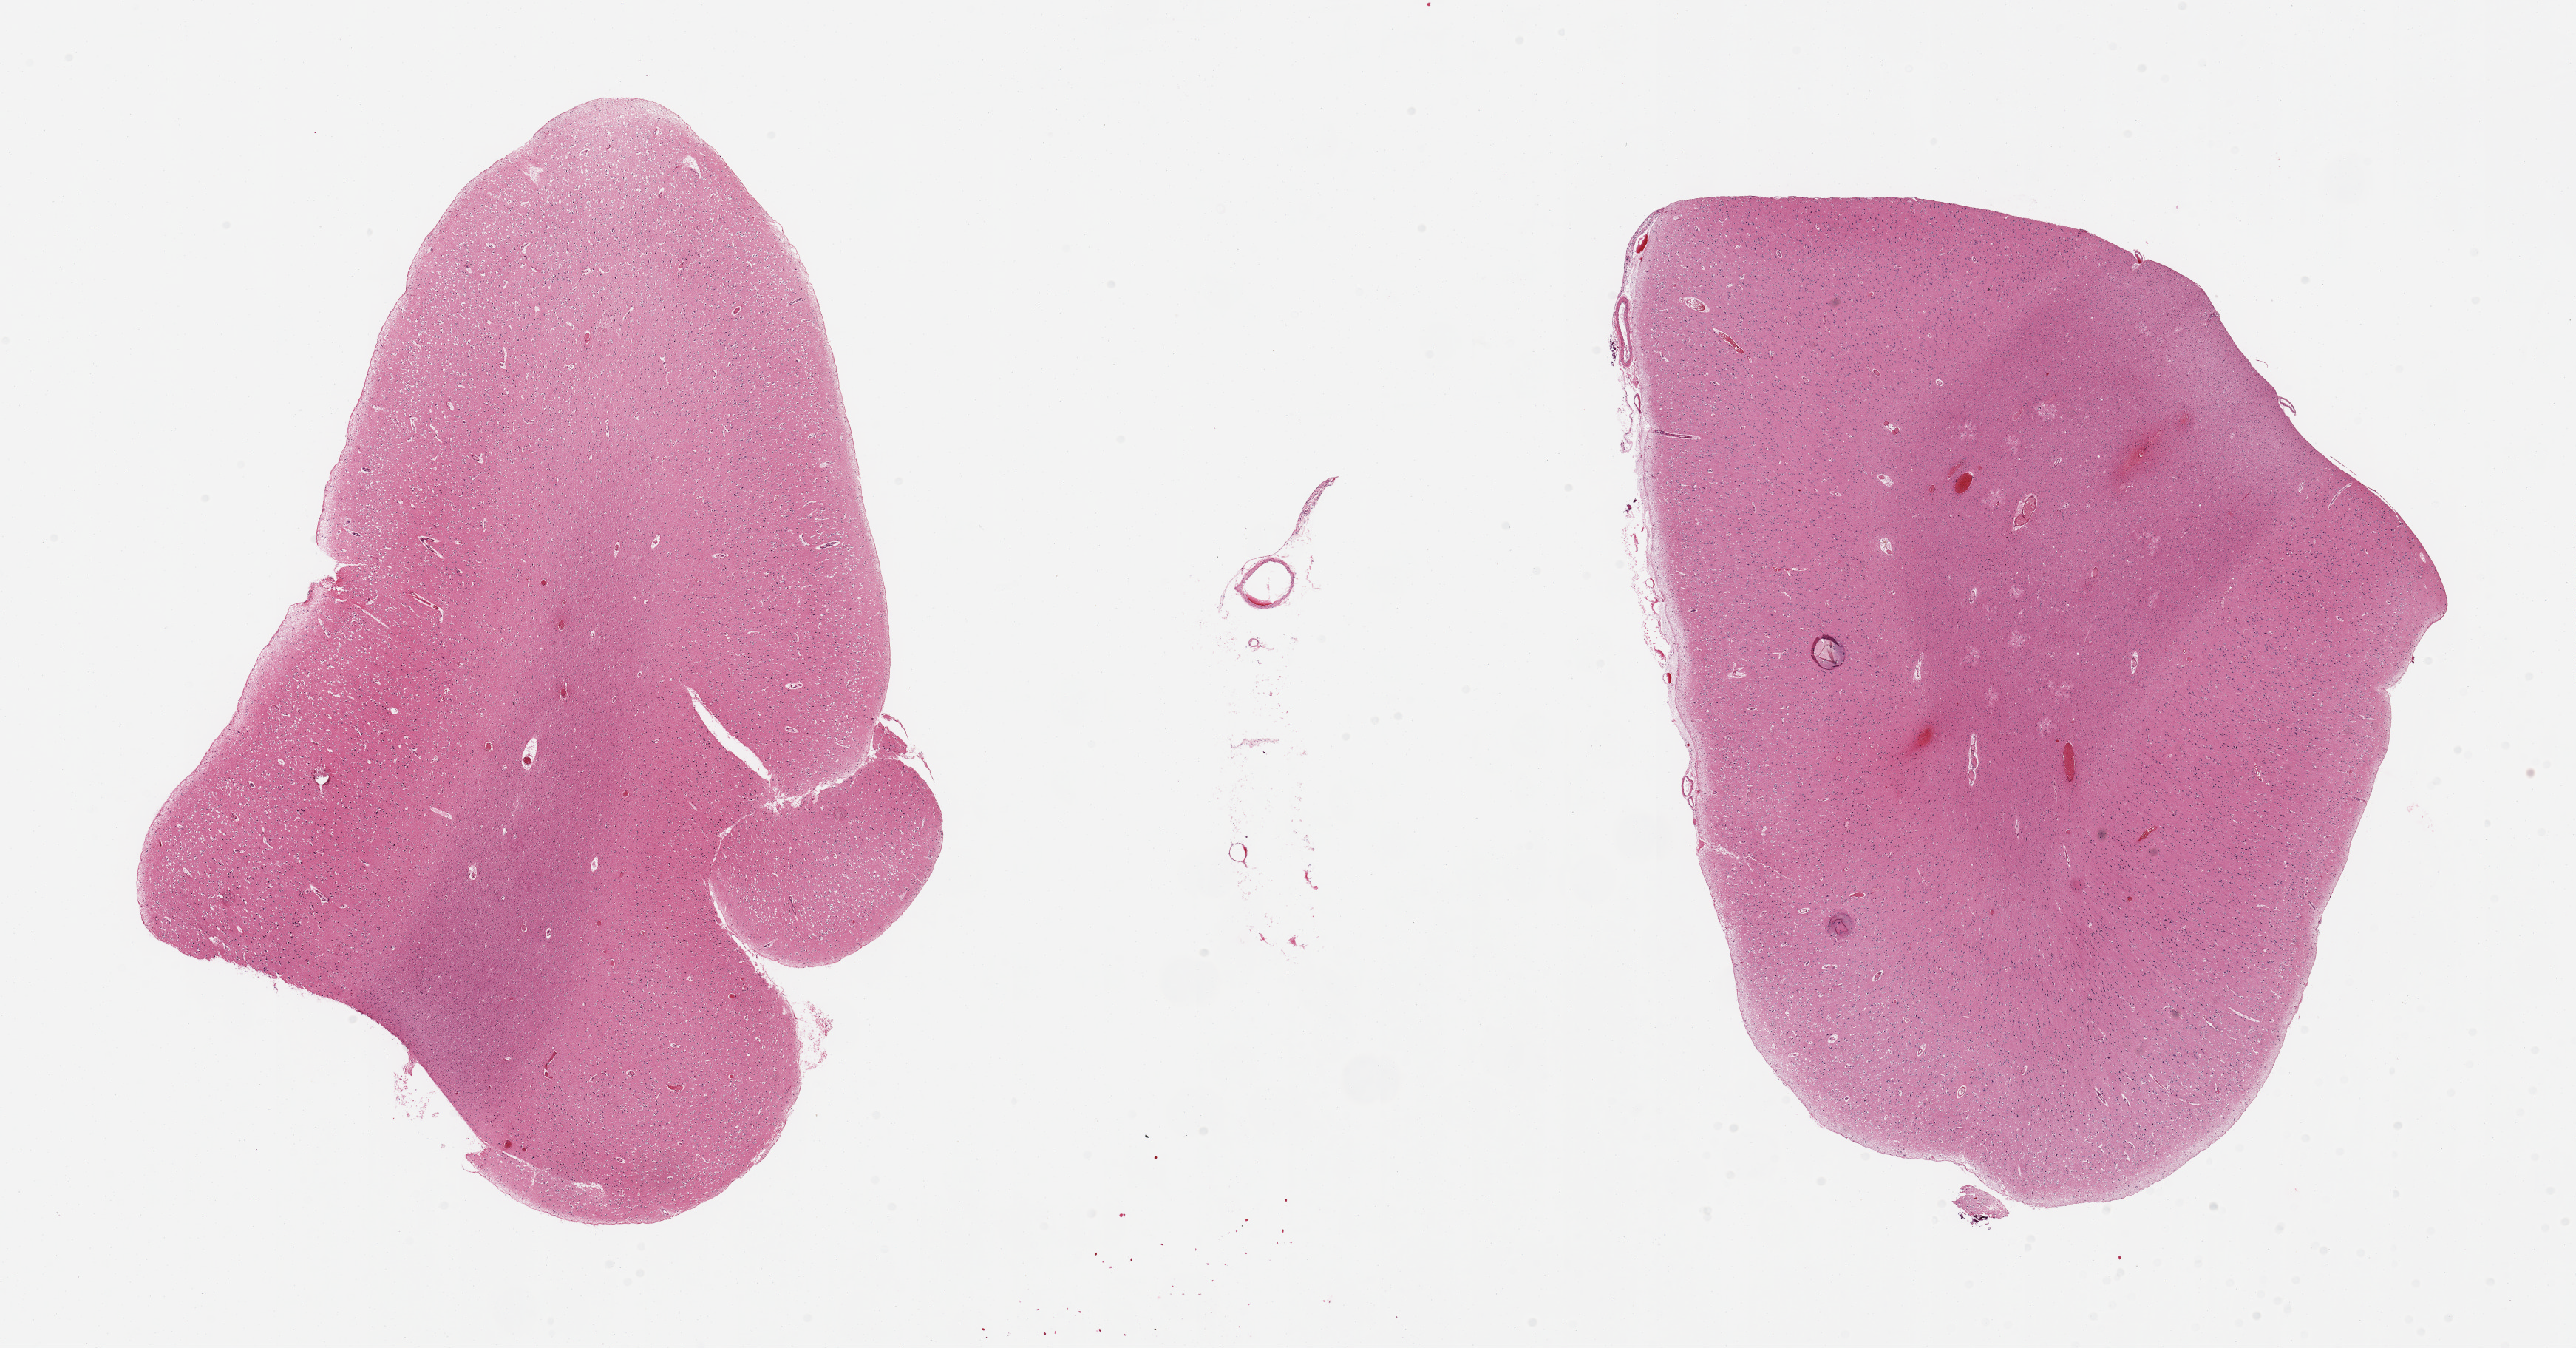
Whole-slide image, H&E stain, whole scanned area (about 27.6 x 14.4 mm) shown as a low-resolution overview, PAXgene-fixed, paraffin-embedded tissue, sampled site (target tissue): cerebral cortex, tissue donor sample. Male donor.
Pathologist's review note for this sample: 2 pieces.